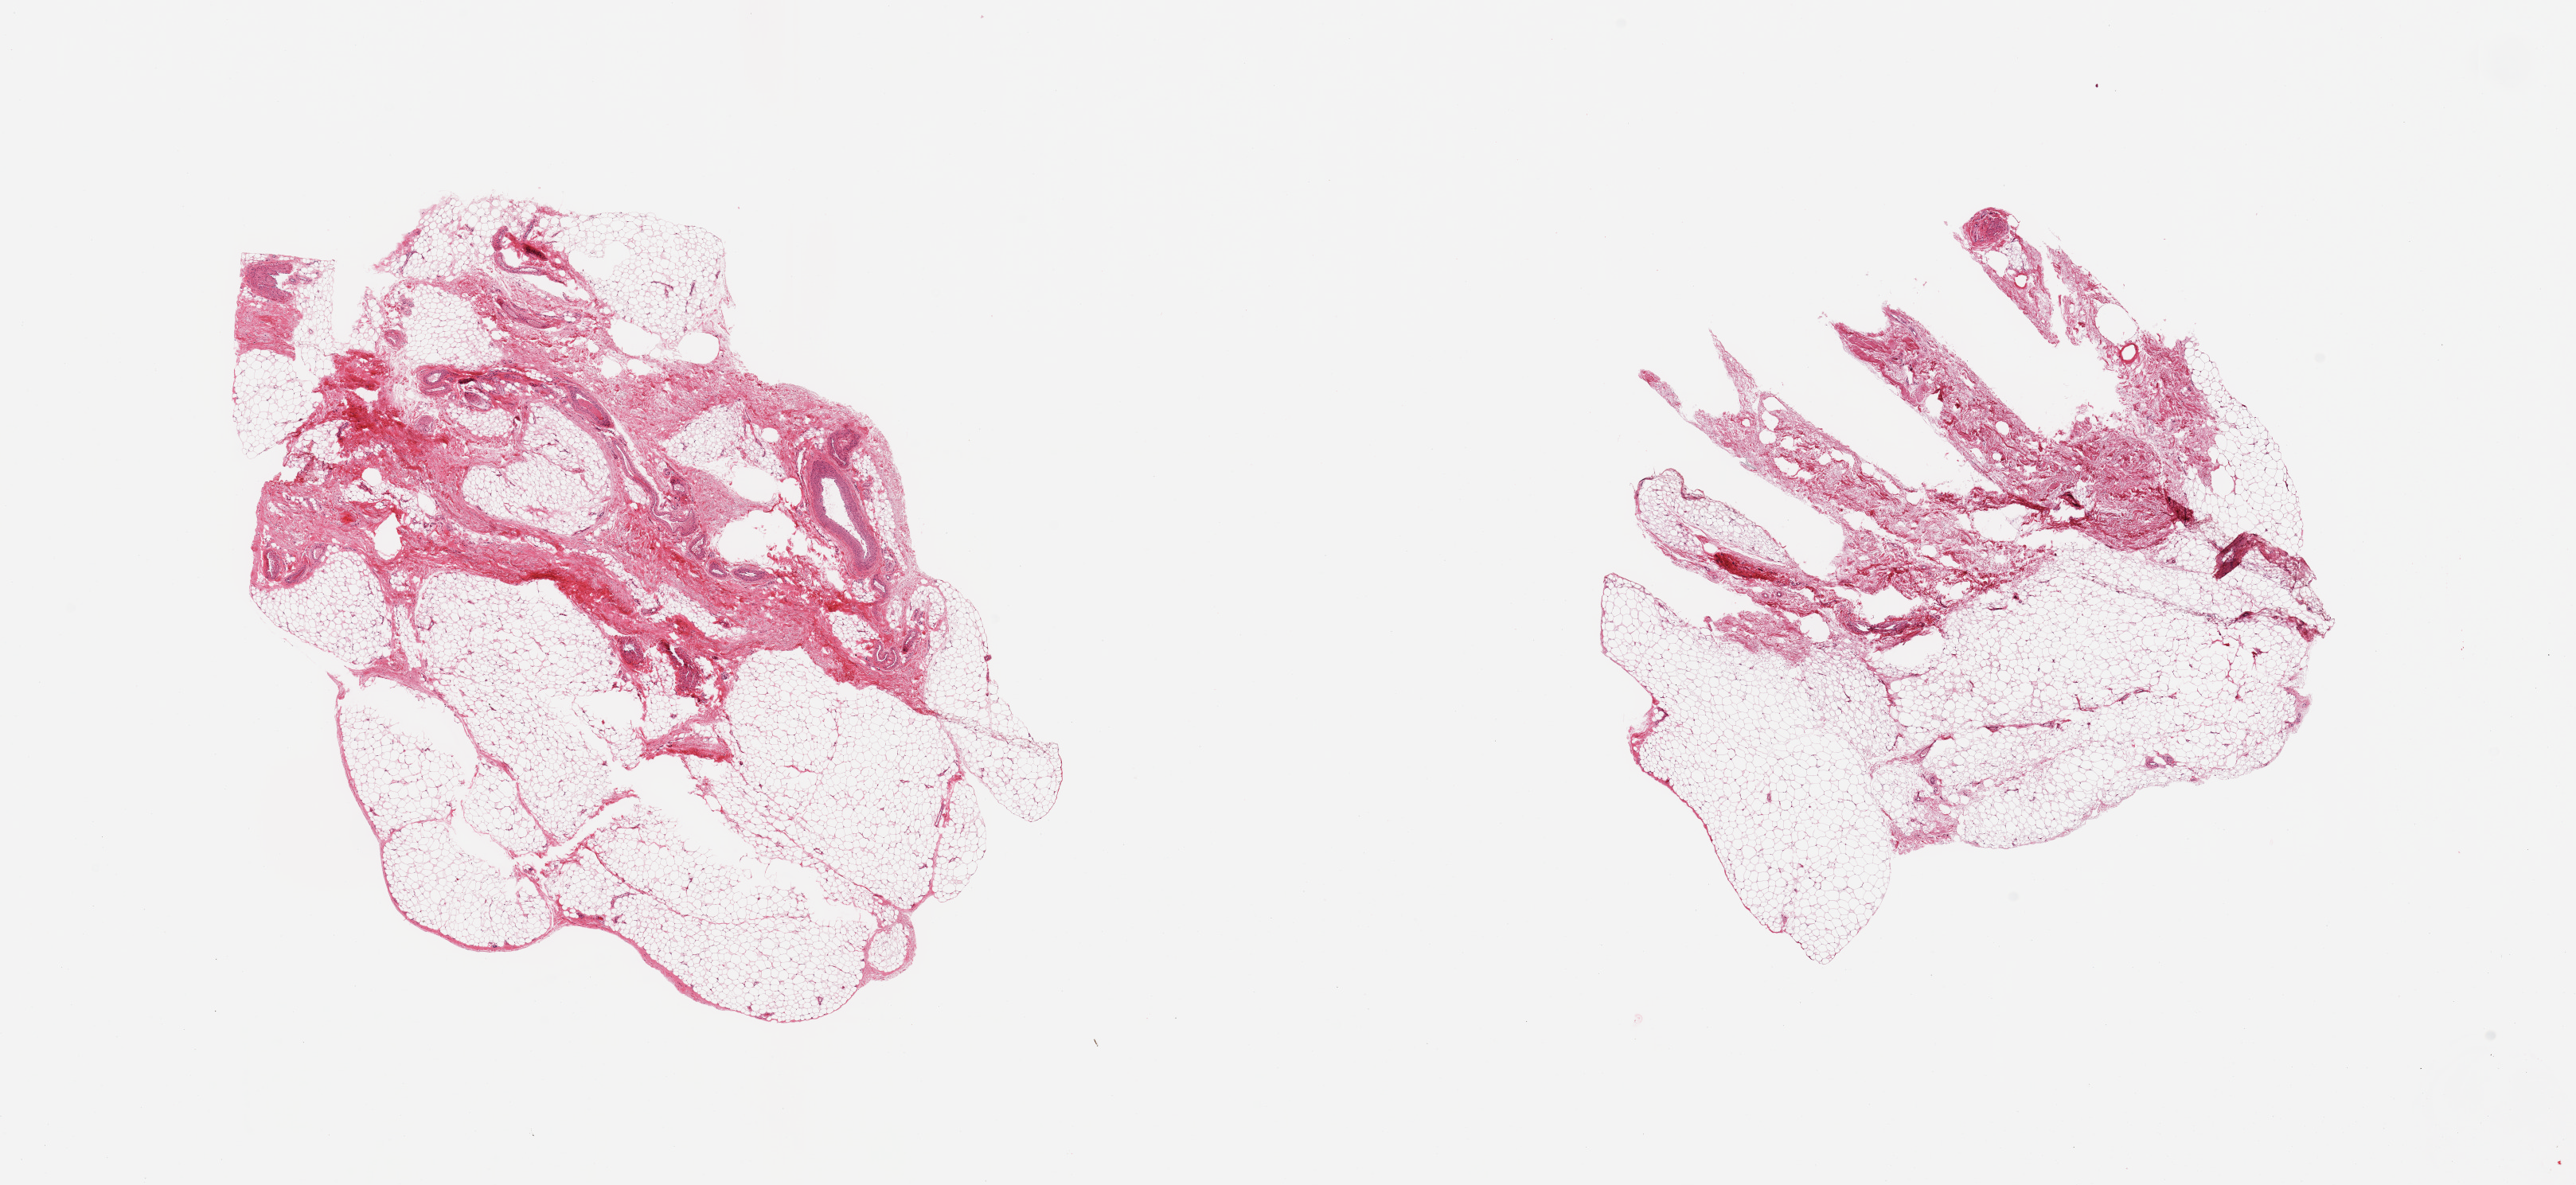
Hematoxylin and eosin (H&E) whole-slide image, a low-resolution overview of the entire scanned area, about 25.6 x 11.8 mm (acquisition: 20x scan); PAXgene-fixed paraffin-embedded (PFPE) section; section of adipose tissue (target tissue); donor tissue sample.
Pathologist's review note for this sample: 2 pieces; 20% fibrous content; deep cassette indentations on 1 piece.